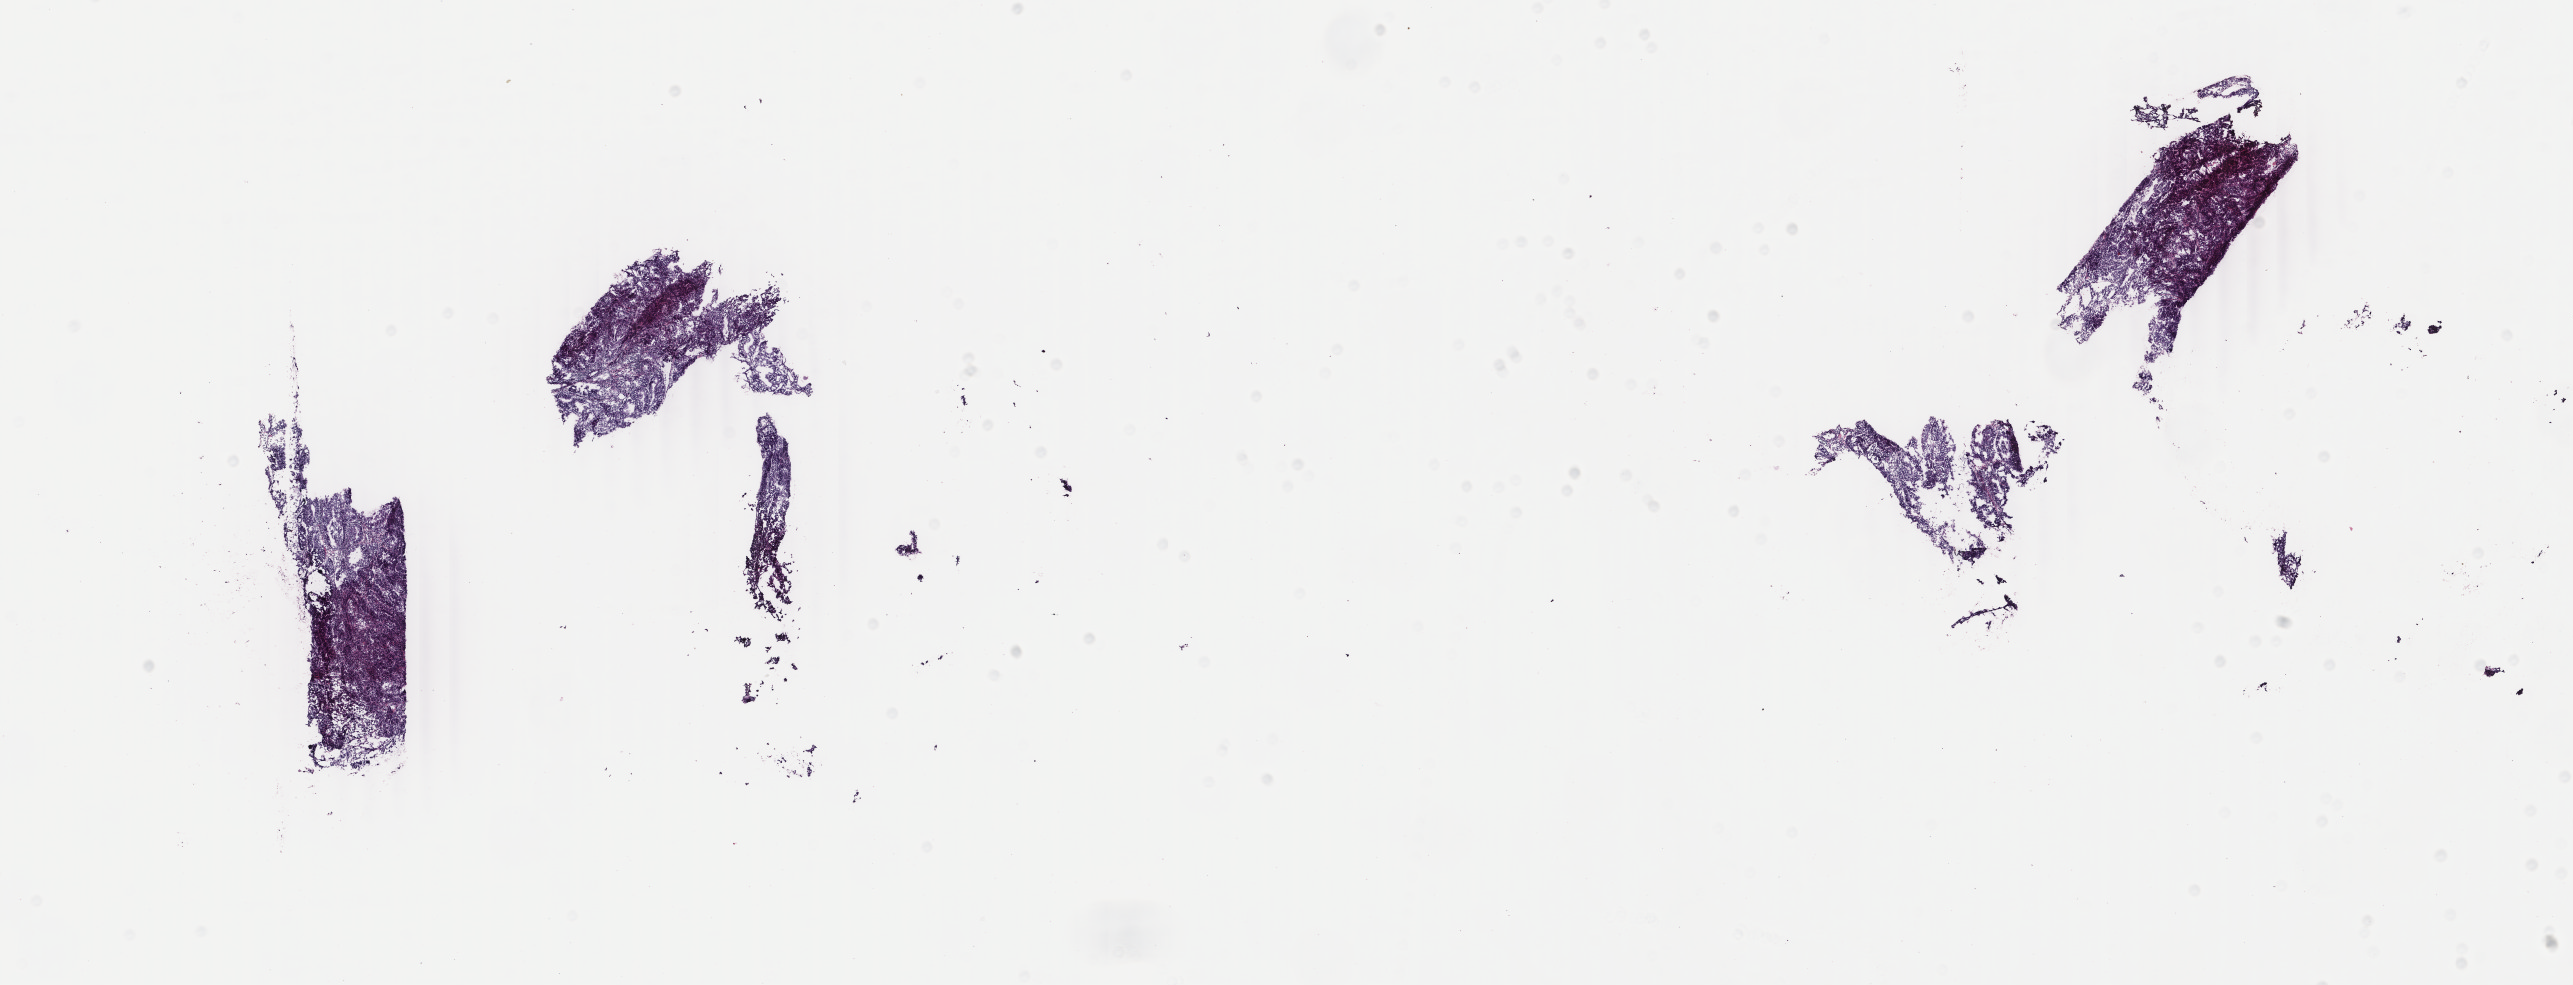
H&E whole-slide image — low-resolution overview of the scanned area, about 20.5 x 7.8 mm (from a 40x scan); frozen section; primary tumour sample from the uterus. Patient: female, age at initial diagnosis 53 years. Histologic grade: G1 (well differentiated). Composition of this section per pathologist review: tumour cells 70%, tumour nuclei 70%, normal cells 0%, stromal cells 20%, necrosis 10%. Inflammatory infiltration, as recorded: lymphocyte infiltration 60%, monocyte infiltration 5%, neutrophil infiltration 30%.
* histologic diagnosis: Endometrioid adenocarcinoma, NOS (endometrium)
* FIGO stage: IA